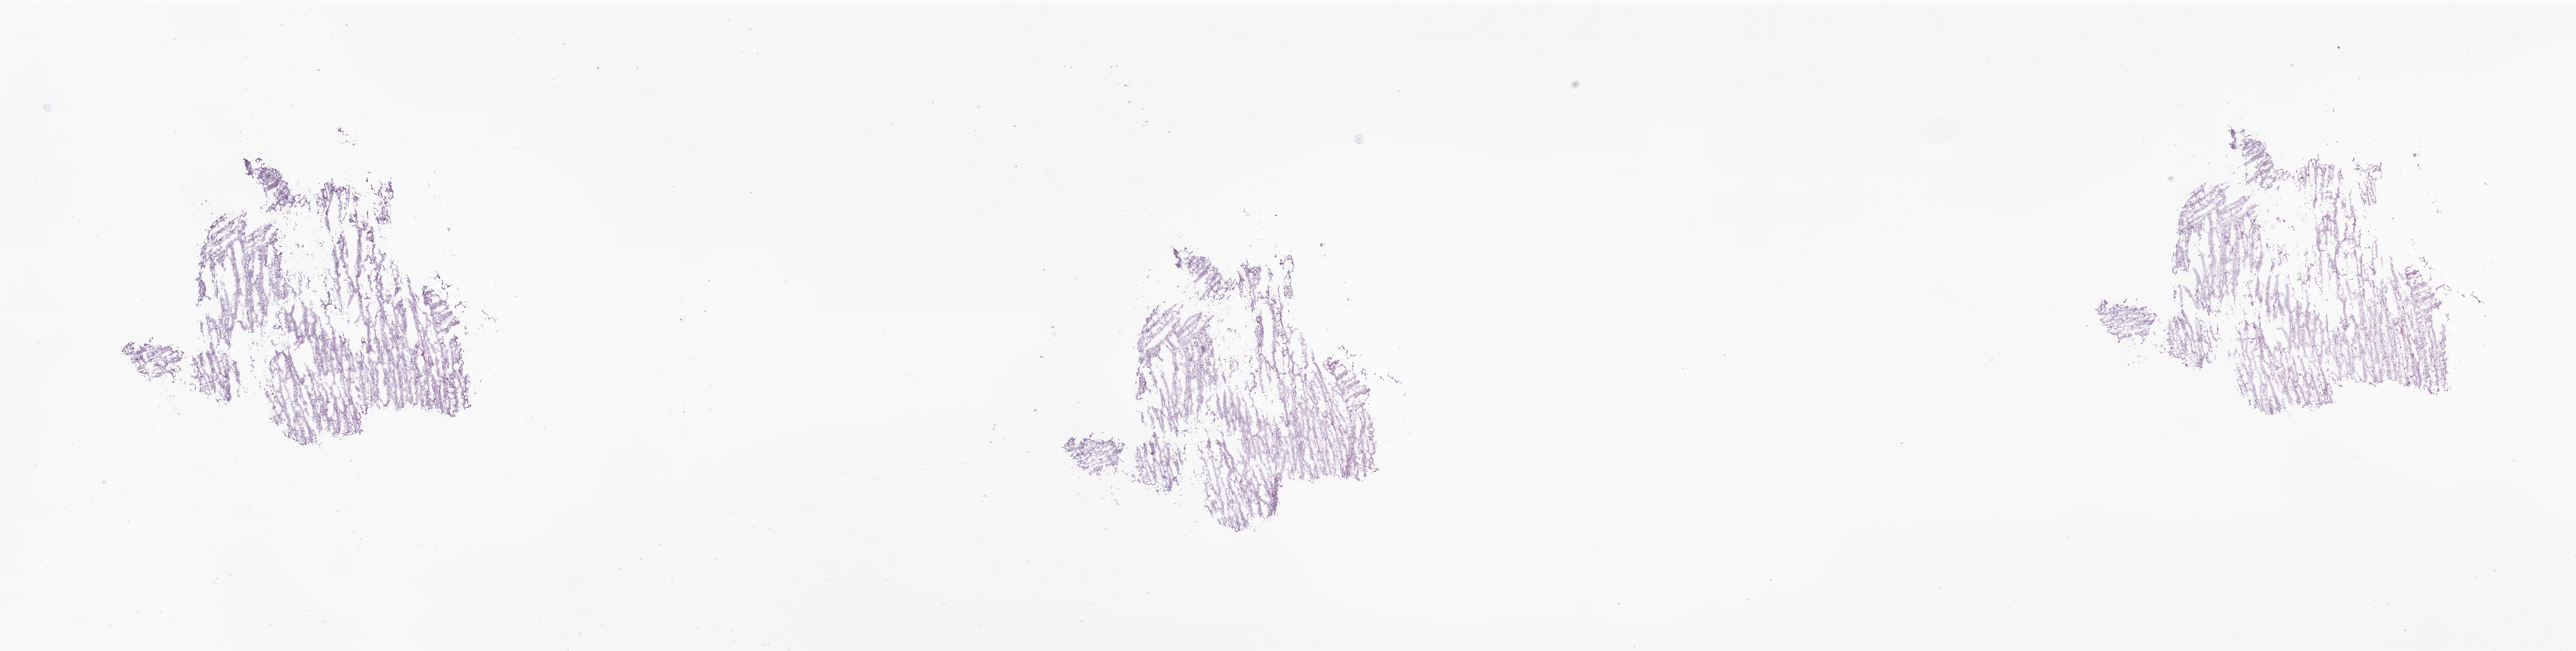
Digitized H&E-stained section of tumor tissue from the frontal lobe, a low-resolution overview of the entire scanned area, about 40.3 x 10.2 mm. Cryosection (OCT / tissue freezing medium). Patient: female, age 184 months (15 years 4 months).
Diagnosis: Glioma, malignant.